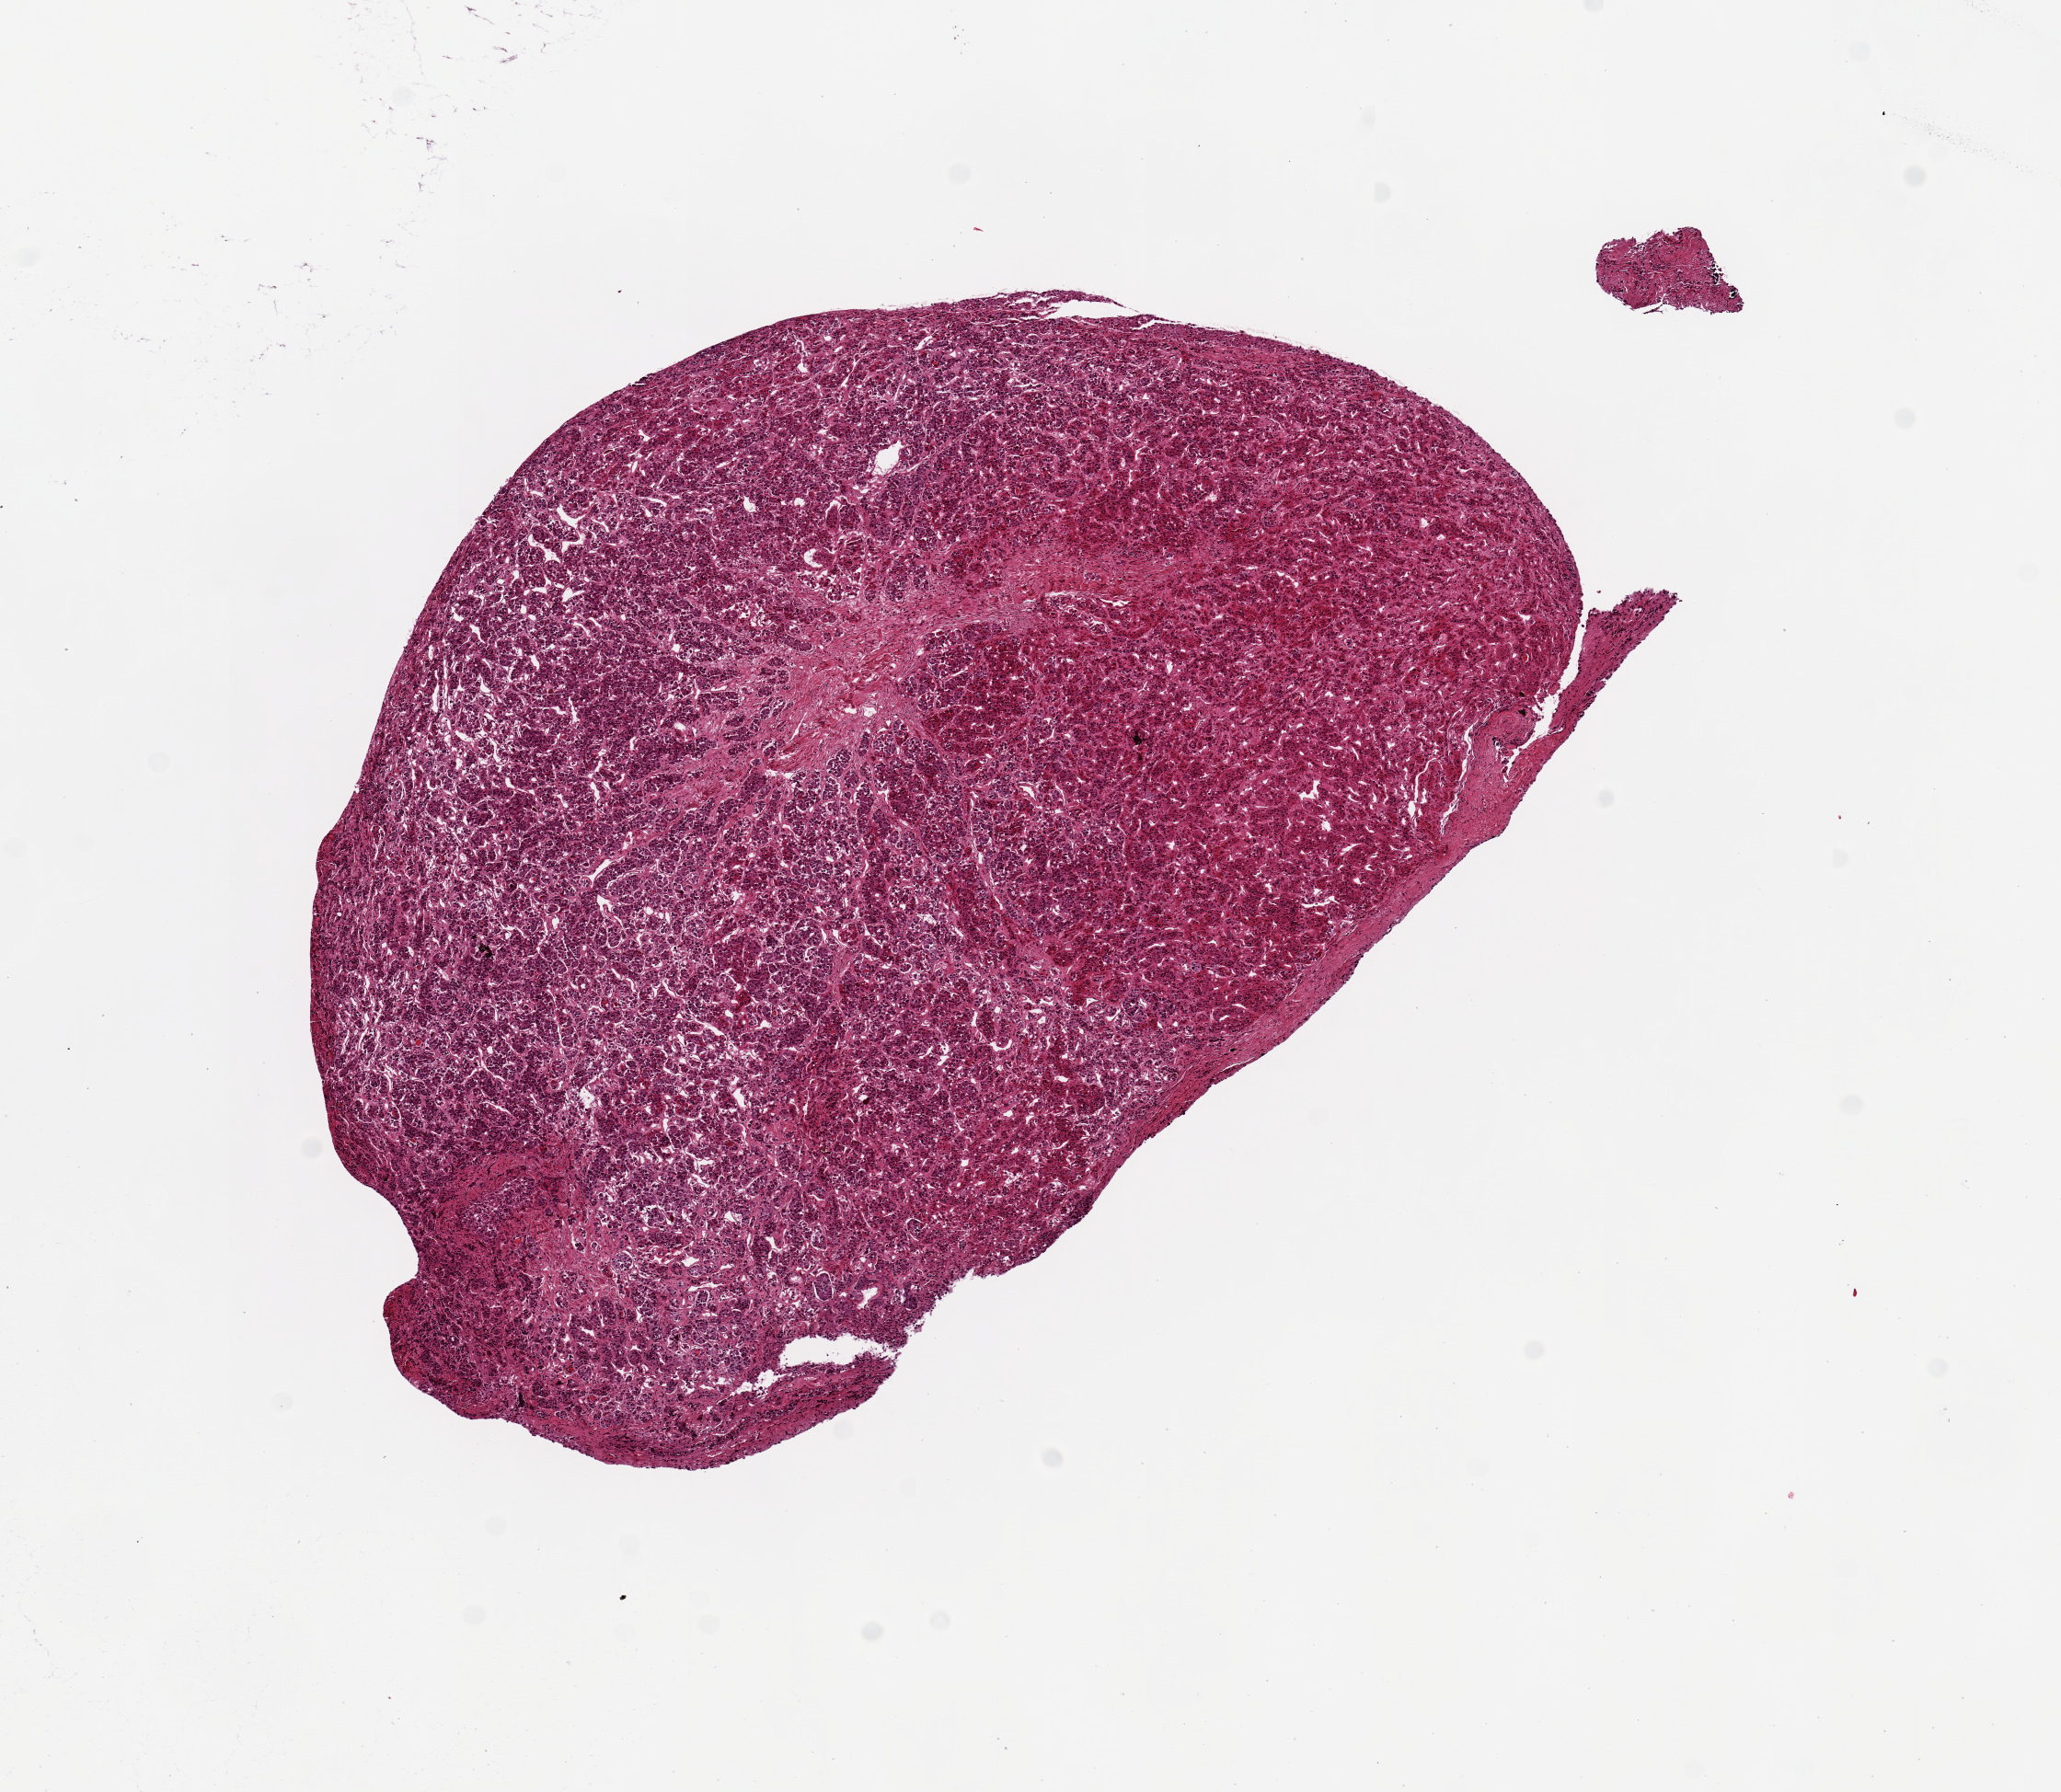
Whole-slide image, haematoxylin and eosin stain, a low-resolution overview of the entire scanned area, about 8.9 x 7.7 mm (from a 20x scan). PAXgene-fixed, paraffin-embedded tissue. Section of pituitary (target tissue). Tissue donor sample. Male donor.
* pathologist's review note for this sample: 6x3.7mm